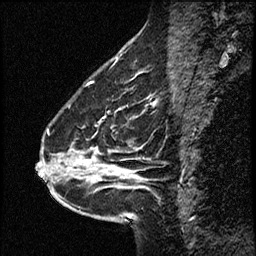
Breast MRI (dynamic contrast-enhanced), one sagittal slice. Slice 21 of 50 in the series (ordered by position). Dynamic contrast-enhanced study with each time point stored as its own series, time point 2 of 4 at this slice position (early post-contrast, ordered by acquisition time). 1.5 T. TE 4.2 ms, TR 17.5 ms. 3 mm slice thickness. 256 × 256 image matrix, field of view 200 × 200 mm. From the clinical record (not read from this slice): setting: breast cancer imaged before/during neoadjuvant chemotherapy.
Annotated regions visible in this slice (semi-automatically segmented with operator editing):
- analysis volume of interest (the breast-tissue region the enhancement analysis was run in; not a lesion): bounding box <52,98,158,207> (left, top, right, bottom; pixels)
- tumour enhancement mask (voxels above the 100 % enhancement threshold inside the analysis volume of interest): <88,161,138,179>